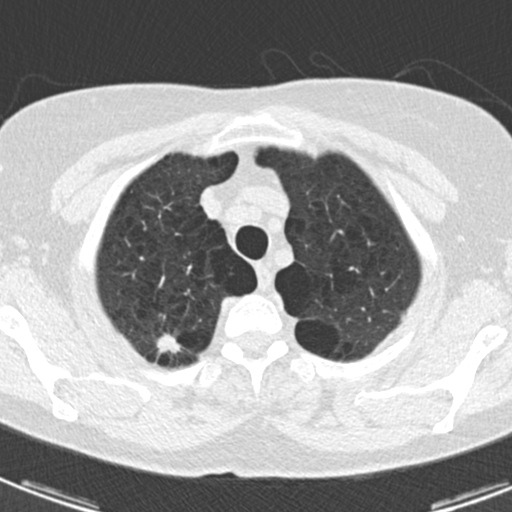
Low-dose screening chest CT, axial slice, third annual screen, lung window (W 1500 / L -600 HU), 2 mm slice thickness, standard (soft-tissue) reconstruction kernel (B30f), slice 22 of 174 in the series. Female, age 59 years at enrolment. Current smoker at enrolment.
Expert reader's lesion annotation, box from (x=132, y=320) to (x=190, y=365) px. Screening reader's record for this exam (one nodule recorded; not confirmed to be the boxed lesion): non-calcified nodule or mass ≥4 mm, right upper lobe, 12 × 7 mm, spiculated (stellate) margins, soft tissue attenuation, pre-existing on the prior screen: yes; interval growth: yes. Official screen result: positive, other. Participant outcome: lung cancer diagnosed 32 days after this screen — adenocarcinoma, NOS, right upper lobe, poorly differentiated (G3), stage IA (AJCC 6th edition), 20 mm at pathology.